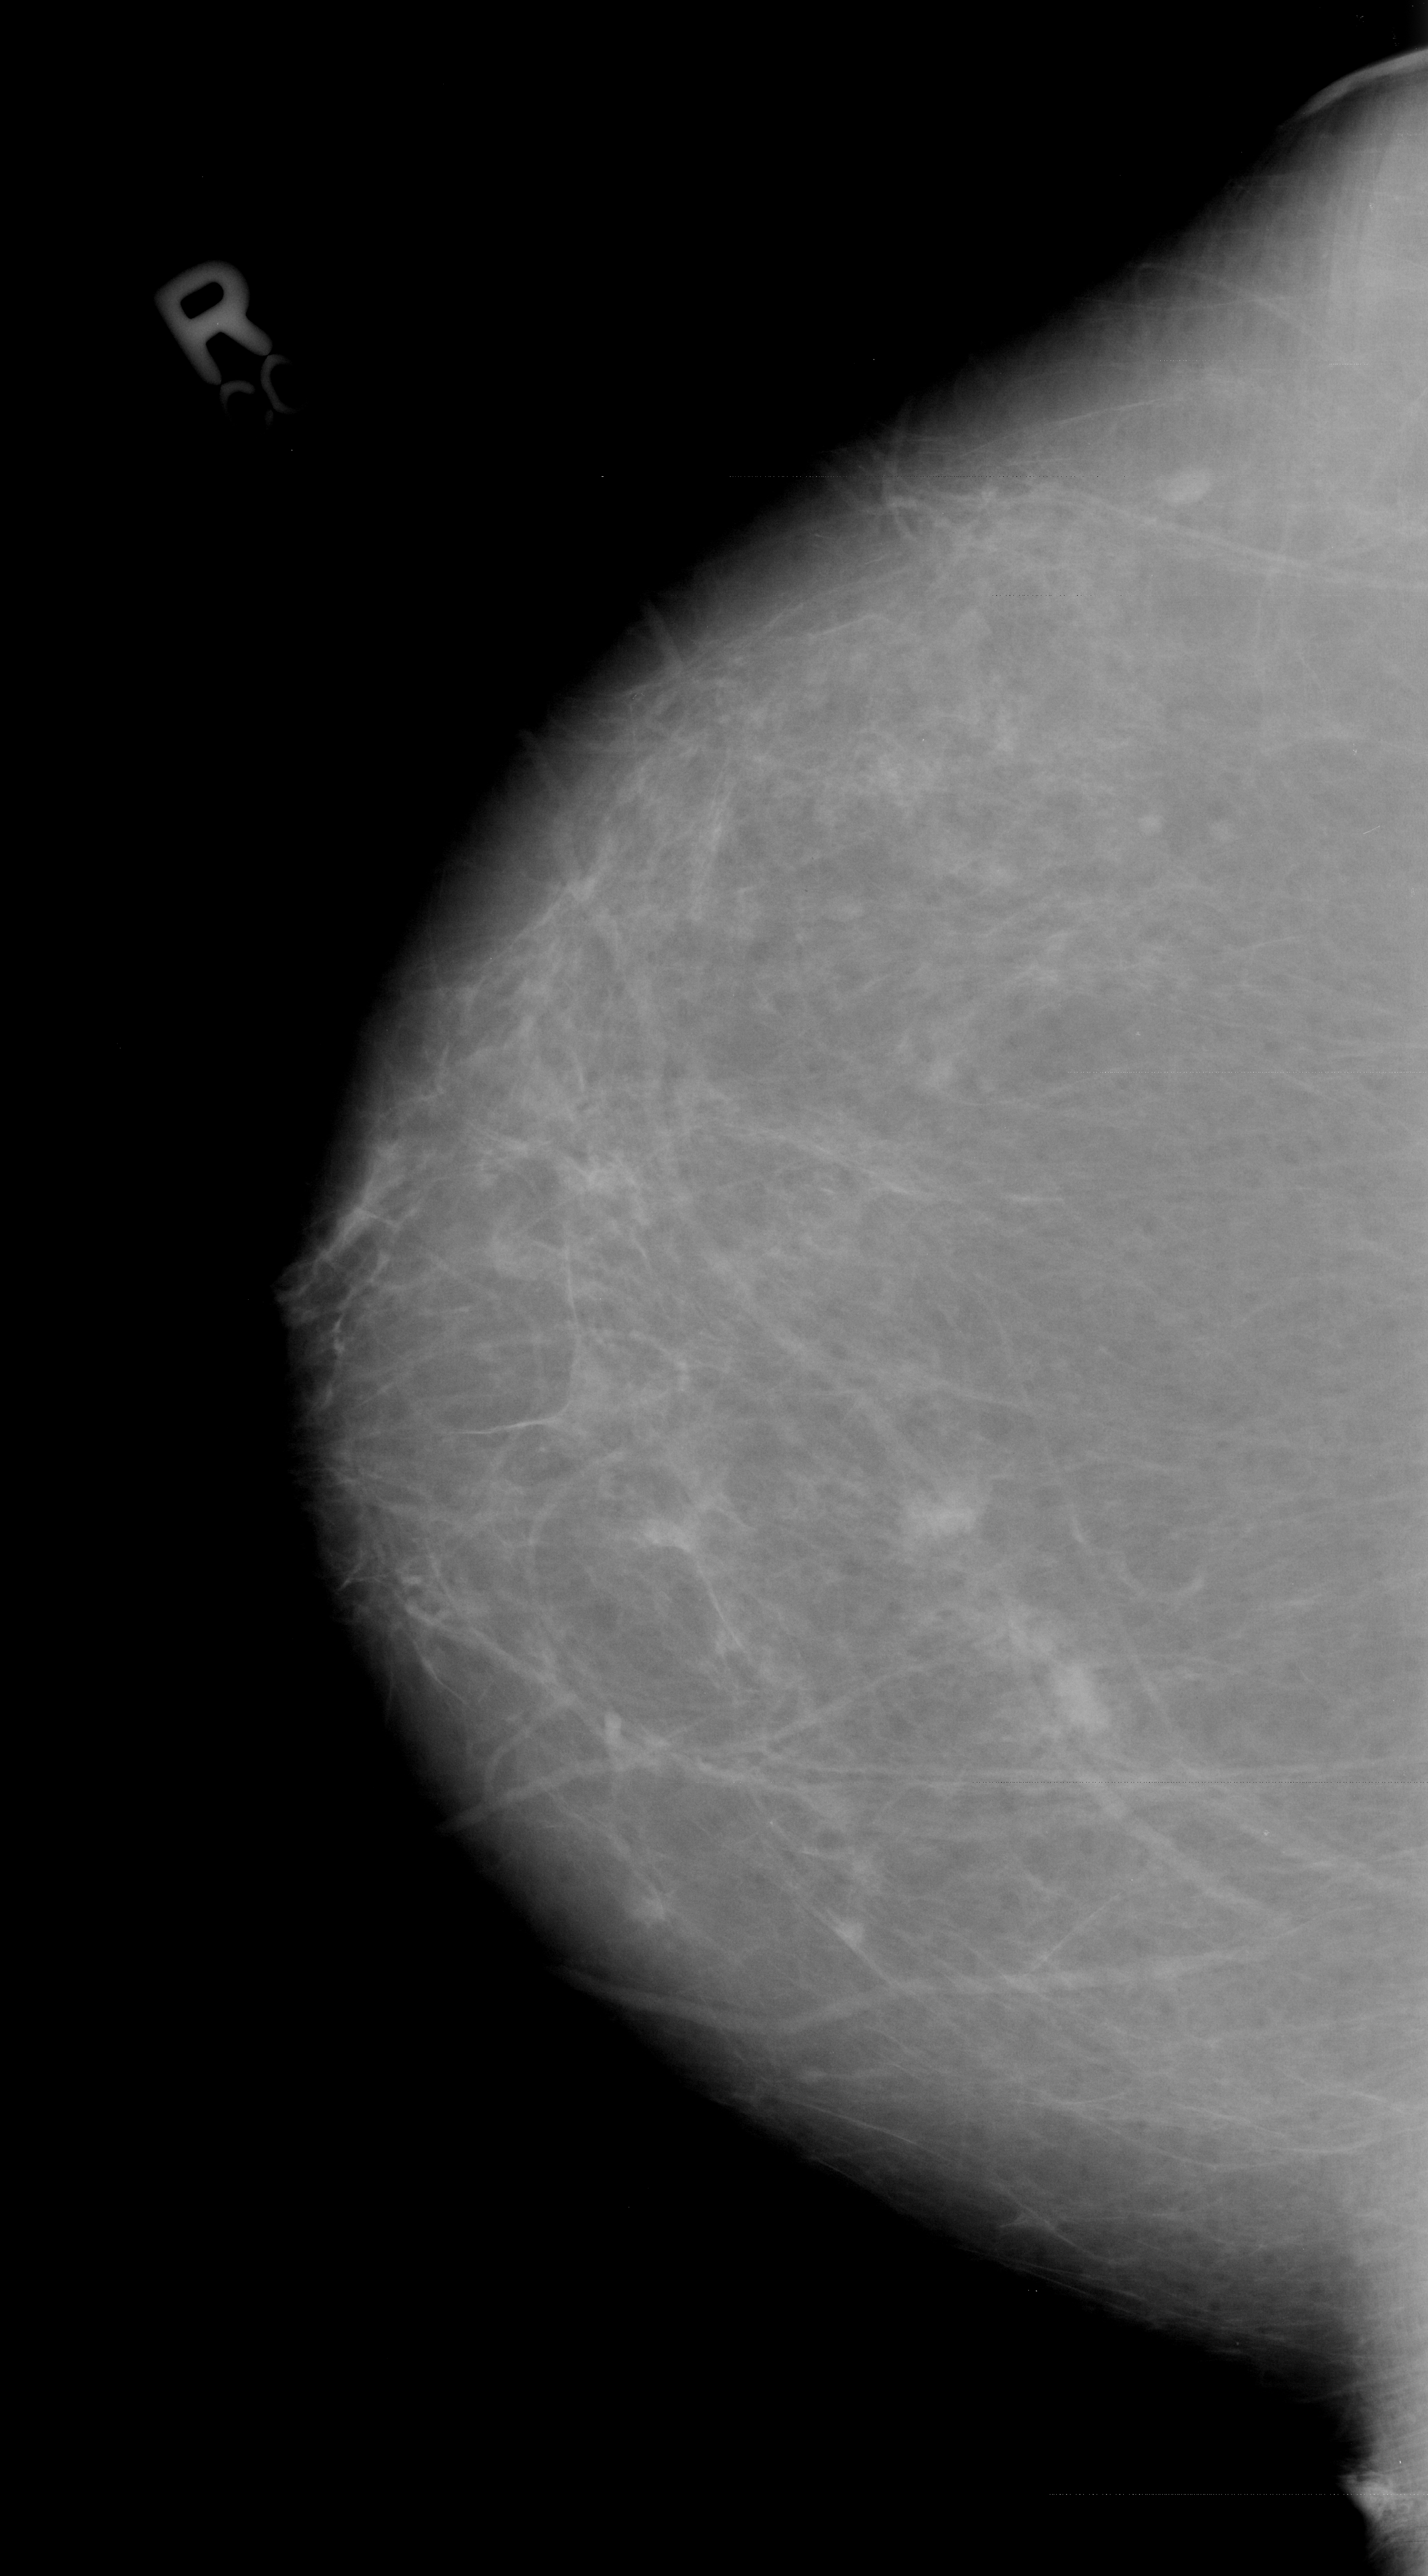
Mammogram (digitized film); right breast; craniocaudal (CC) view; BI-RADS breast density category 1 (scale 1–4); 1428 × 2576 image matrix.
Expert-marked regions of interest on this film, with their recorded descriptors:
- Finding 1 of 2: mass, shape irregular, margins ill defined; BI-RADS assessment category 4; pathology result (as recorded, not read from the image): malignant: bounding box (x1, y1, x2, y2) in pixels: (882, 1482, 986, 1566)
- Finding 2 of 2: mass, shape irregular, margins ill defined; BI-RADS assessment category 4; subtlety rating 3 on a 1 (subtle) to 5 (obvious) scale; pathology result (as recorded, not read from the image): malignant: (1038, 1650, 1116, 1740)